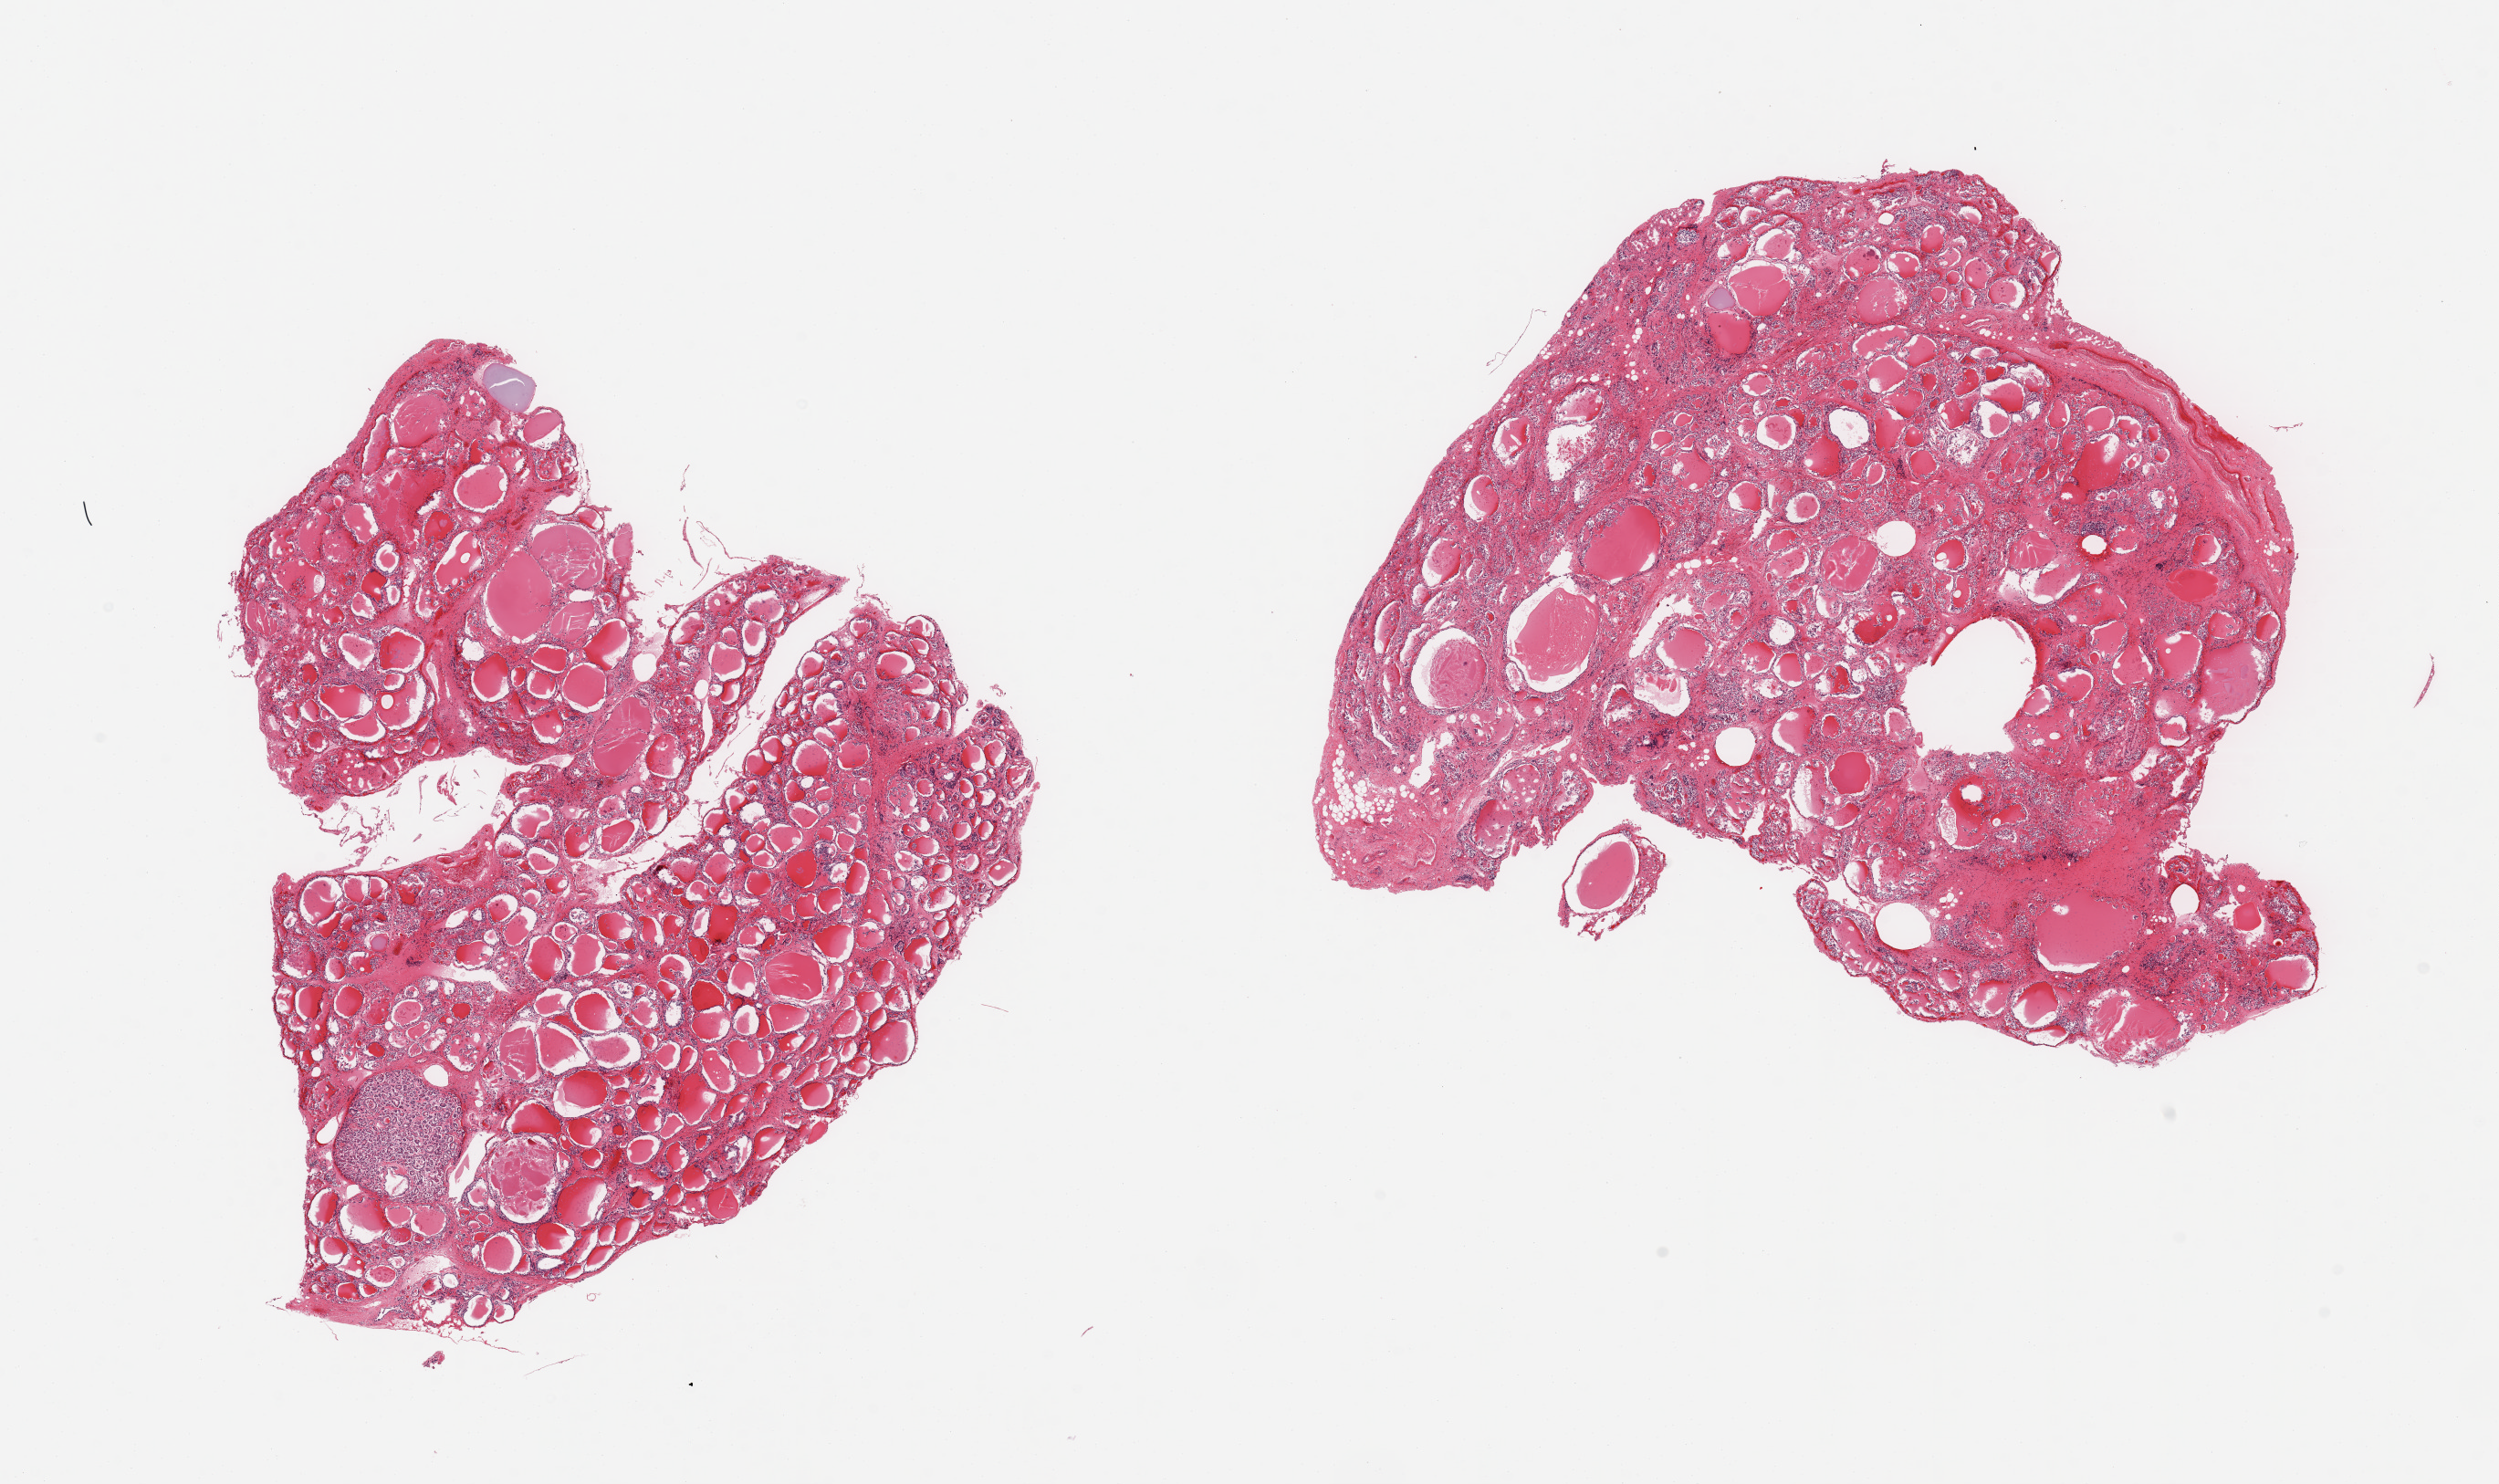
Digitized H&E-stained section, whole scanned area (about 21.7 x 12.9 mm, acquisition: 20x scan) shown as a low-resolution overview. PAXgene-fixed, paraffin-embedded tissue. Sampled site (target tissue): thyroid. Donor tissue sample. Male donor.
- reviewer comment on this tissue sample: 2 pieces; small ~ 1mm in diameter well circumscribed likely adenomatous nodule, some interstitial fibrosis, variably sized follicles